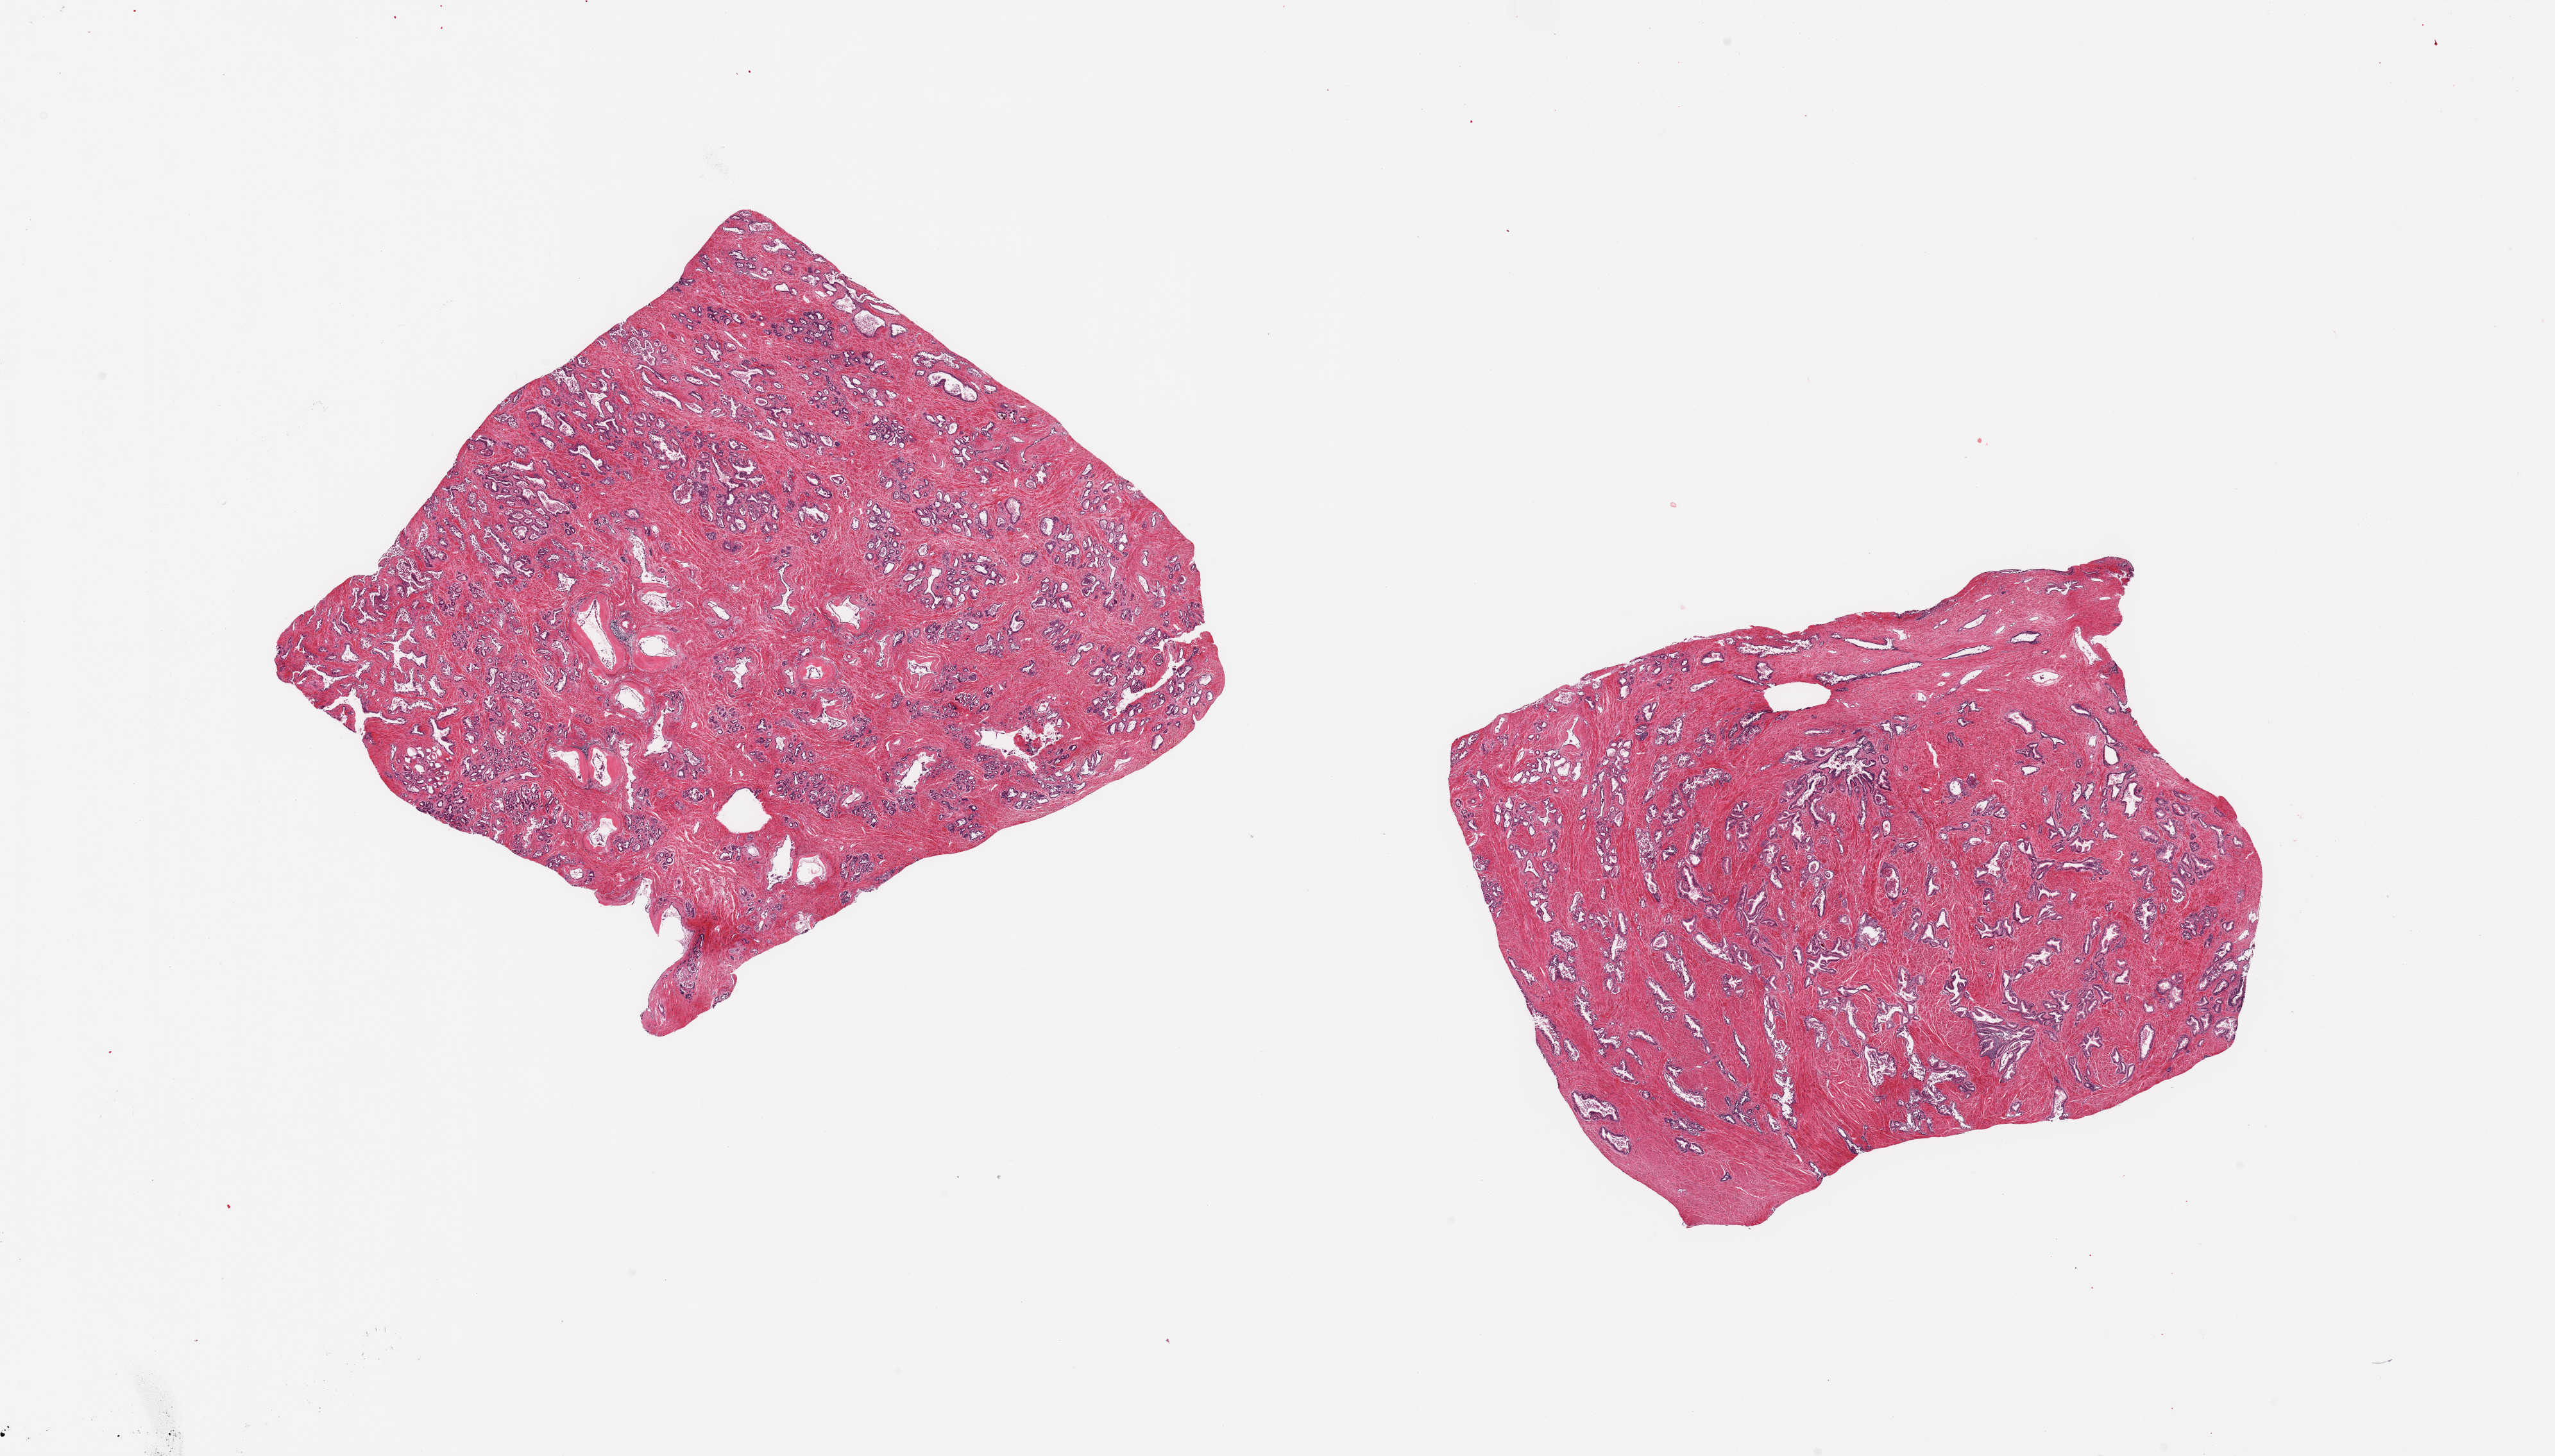
H&E whole-slide image, whole scanned area (about 31.5 x 18.0 mm) shown as a low-resolution overview; PAXgene-fixed, paraffin-embedded tissue; target tissue: prostate; tissue donor sample. Male donor.
Pathologist's review note for this sample: 2 pieces; stroma well preserved.